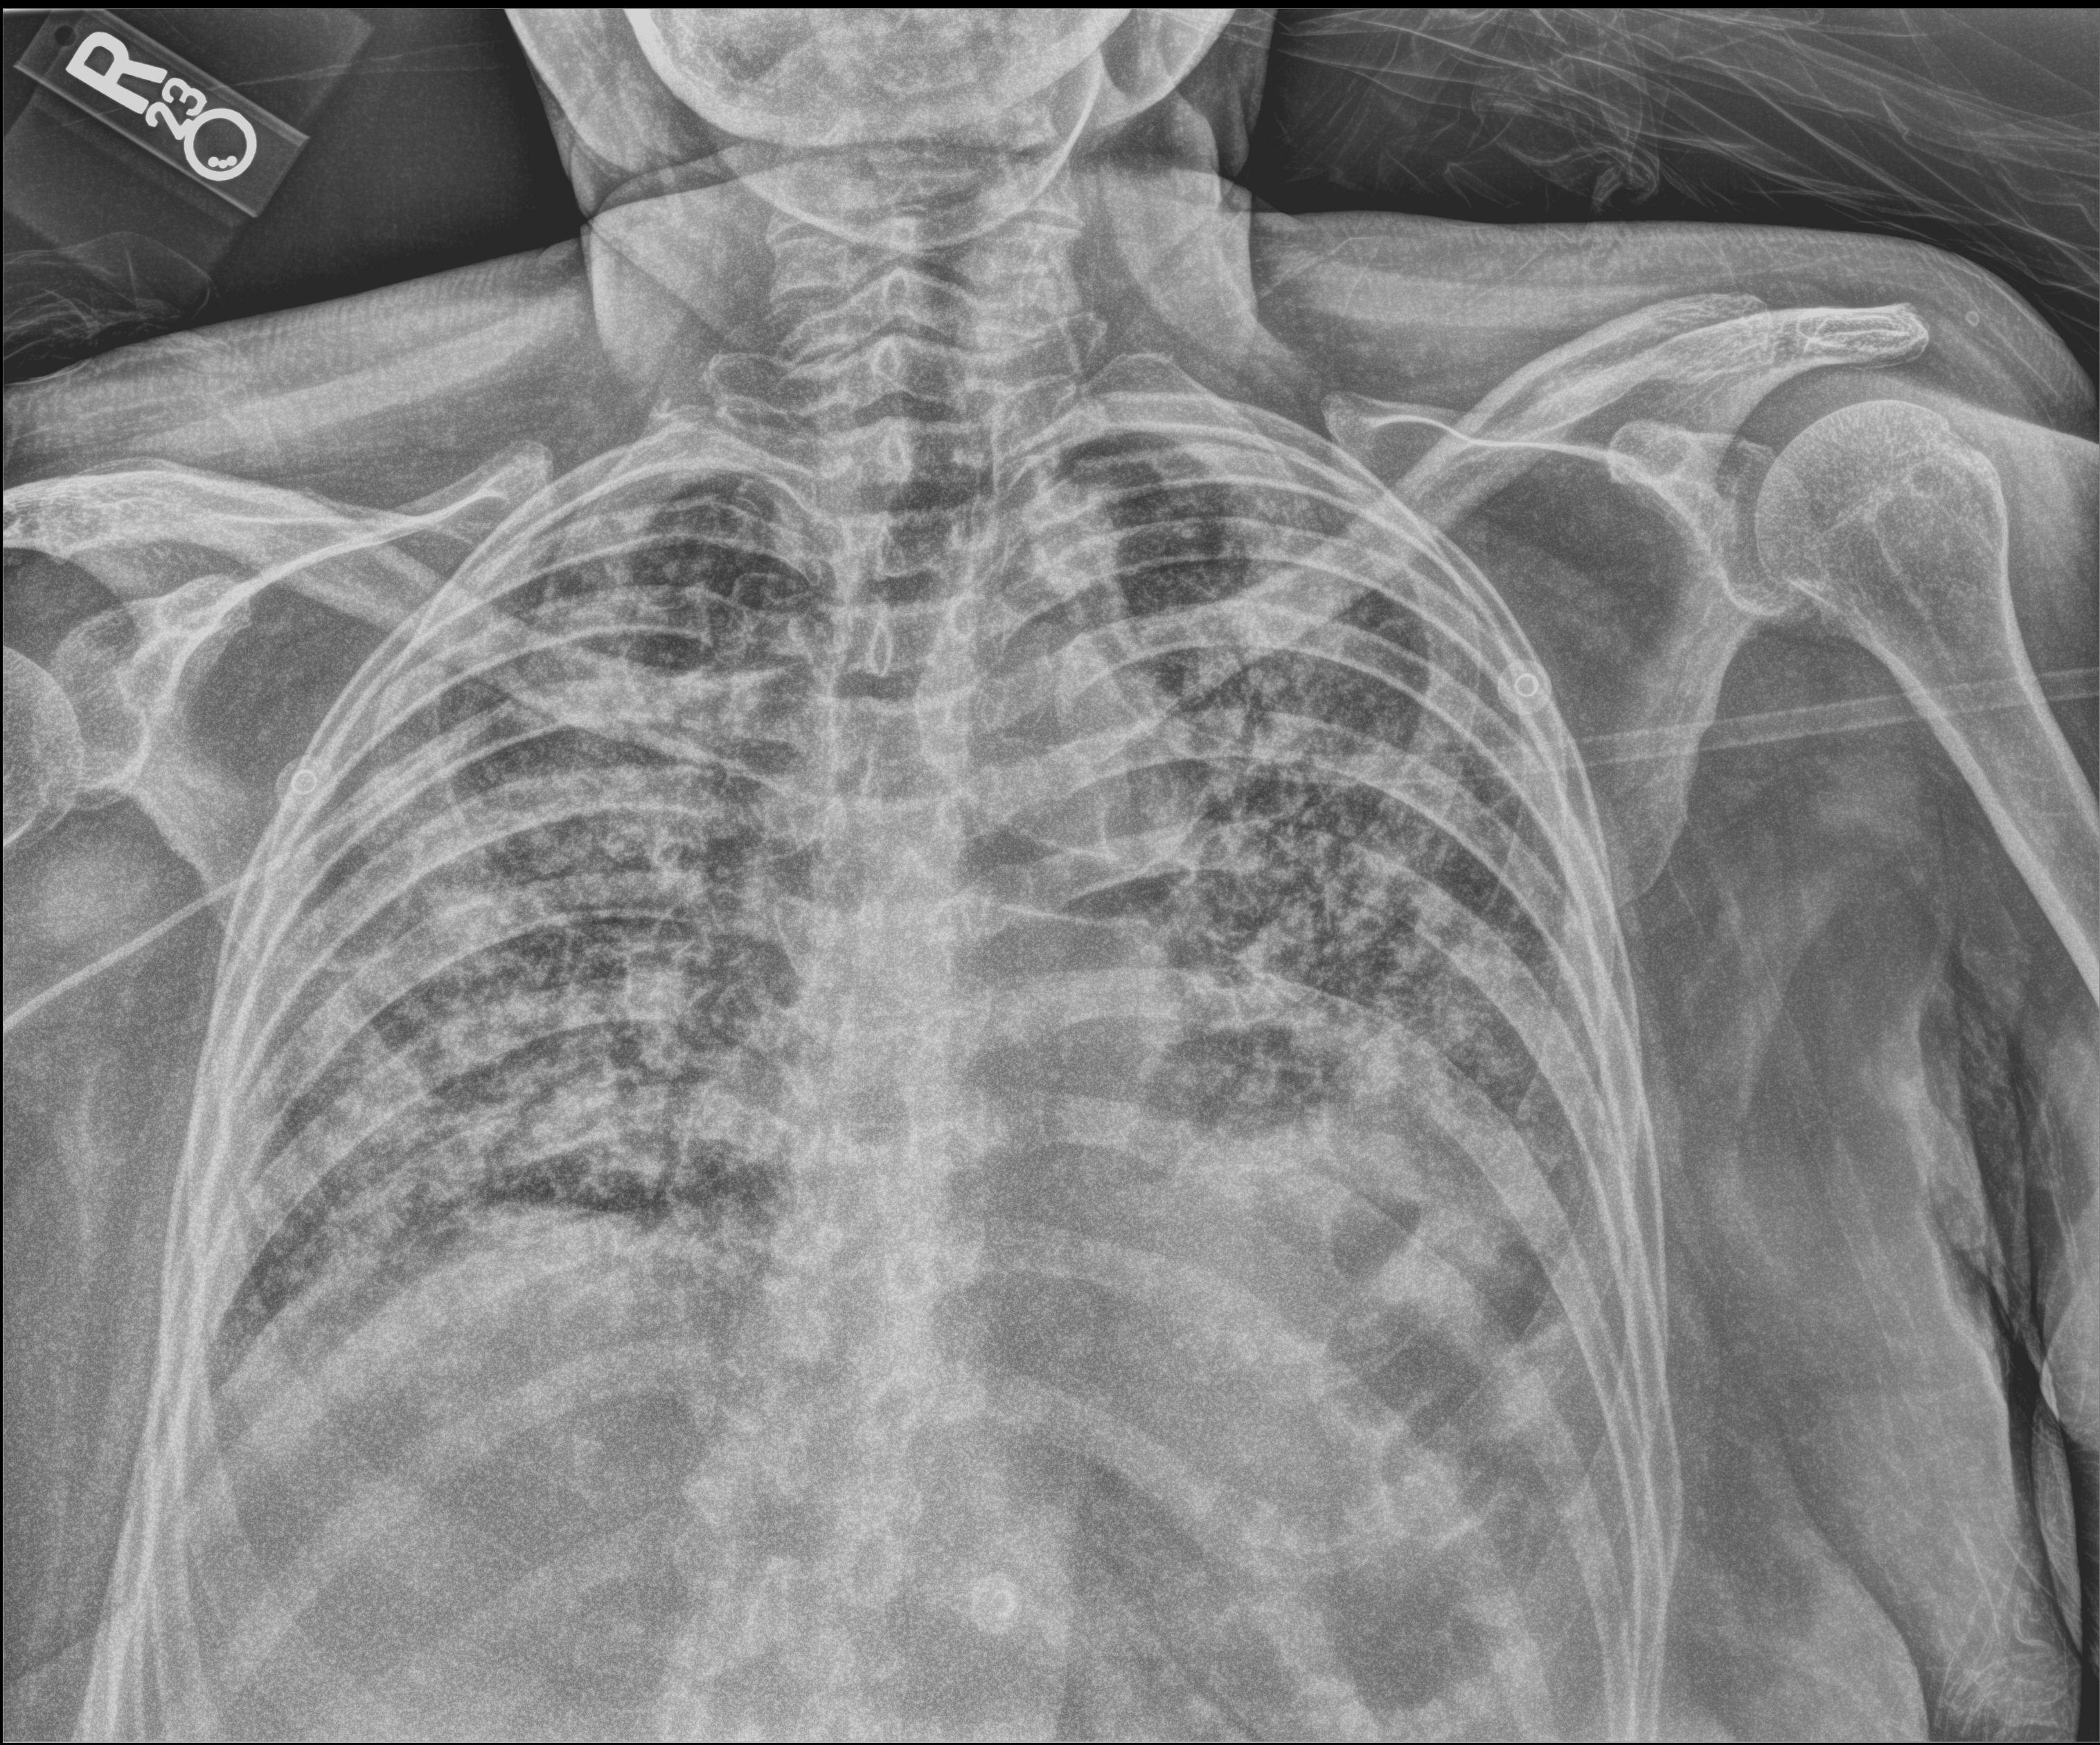
Portable chest radiograph, anteroposterior (AP) projection. Patient hospitalised with COVID-19; female, aged 75–90 years.
Hospital-stay facts (about this admission, not read from this image; timing relative to this image not recorded):
- mechanically ventilated during this hospital stay: yes
- admitted to intensive care during this hospital stay: yes
- chronic kidney disease (admission record): no